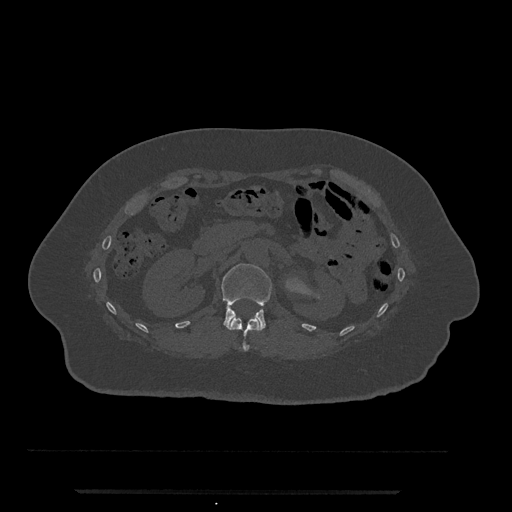
CT including the spine, one axial slice. Slice 129 of 797 in the series (ordered by position). Reconstruction kernel Br40s/3. 120 kVp. Bone window (W 1800 / L 400 HU). 0.5 mm slice thickness. 512 × 512 image matrix, field of view 440 × 440 mm. Patient: female, 51 years. From the clinical record (not read from this slice): primary cancer: neuro; vertebrae with lytic lesions (as recorded): T8.
Outlined on this slice (semi-automatic segmentation, software-assisted and operator-edited):
- L1 vertebra: box from (x=221, y=263) to (x=272, y=329) px
- T12 vertebra: (x=227, y=317)–(x=262, y=351)